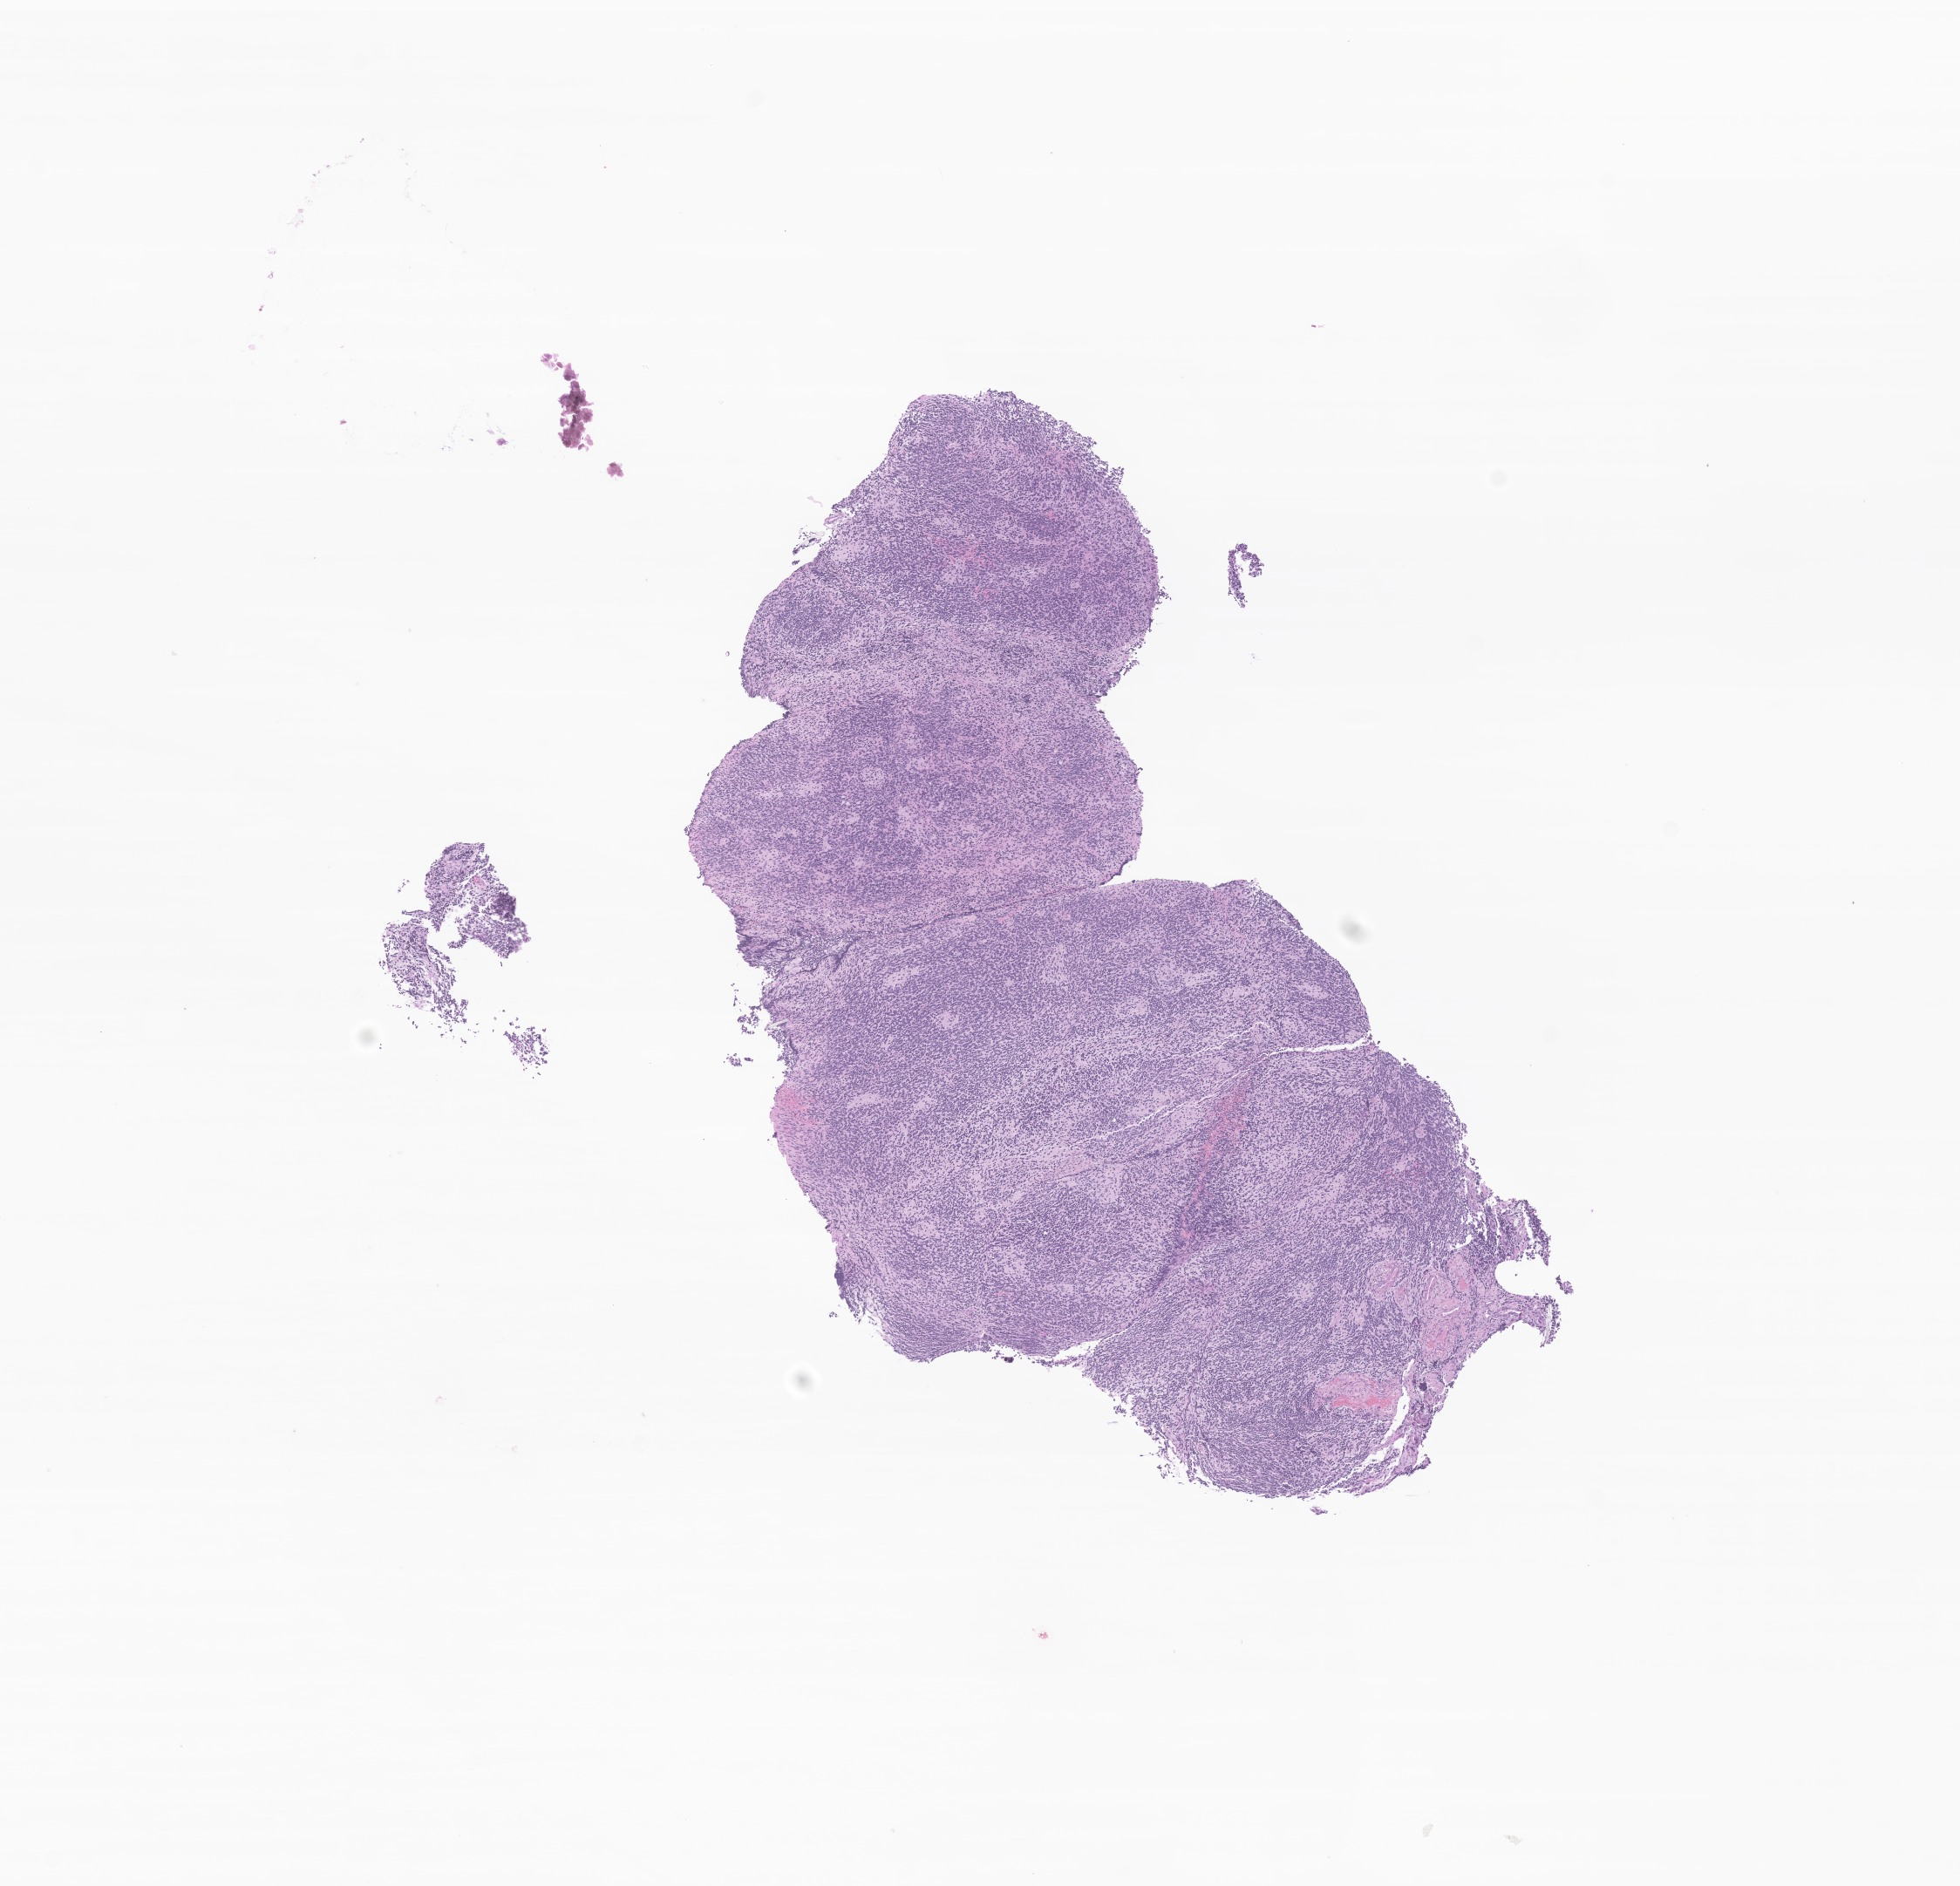
Whole-slide image, haematoxylin and eosin stain of tumor tissue from the brain — low-resolution overview of the scanned area, about 9.5 x 9.1 mm; FFPE section. Male patient, age 147 months (12 years 3 months).
- diagnosis: Medulloblastoma, NOS